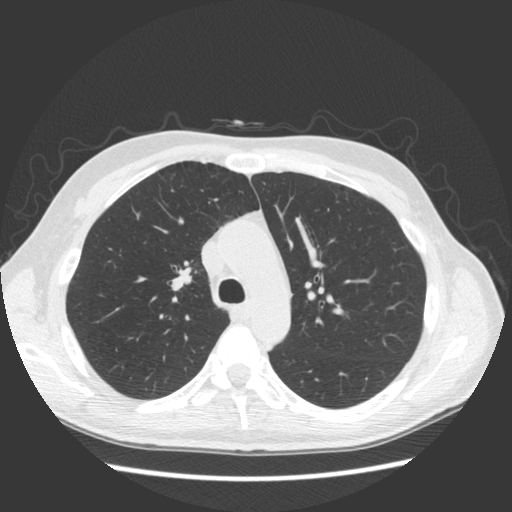
Chest CT (low-dose screening protocol), one axial image; second annual screen; lung window (W 1500 / L -600 HU); 120 kVp. Male, age 57 years at enrolment. Former smoker at enrolment.
Expert-annotated lung lesion, bounding box [x1, y1, x2, y2] px = [153, 248, 204, 300]. The screening reader recorded 3 non-calcified nodules or masses ≥4 mm on this exam (right middle lobe, right middle lobe, right middle lobe); which of them this box marks is not recorded. Official screen result: negative screen, minor abnormalities not suspicious for lung cancer. Lung cancer was diagnosed 264 days after this screen: adenocarcinoma, NOS, right upper lobe, poorly differentiated (G3), stage IB (AJCC 6th edition), 25 mm at pathology.